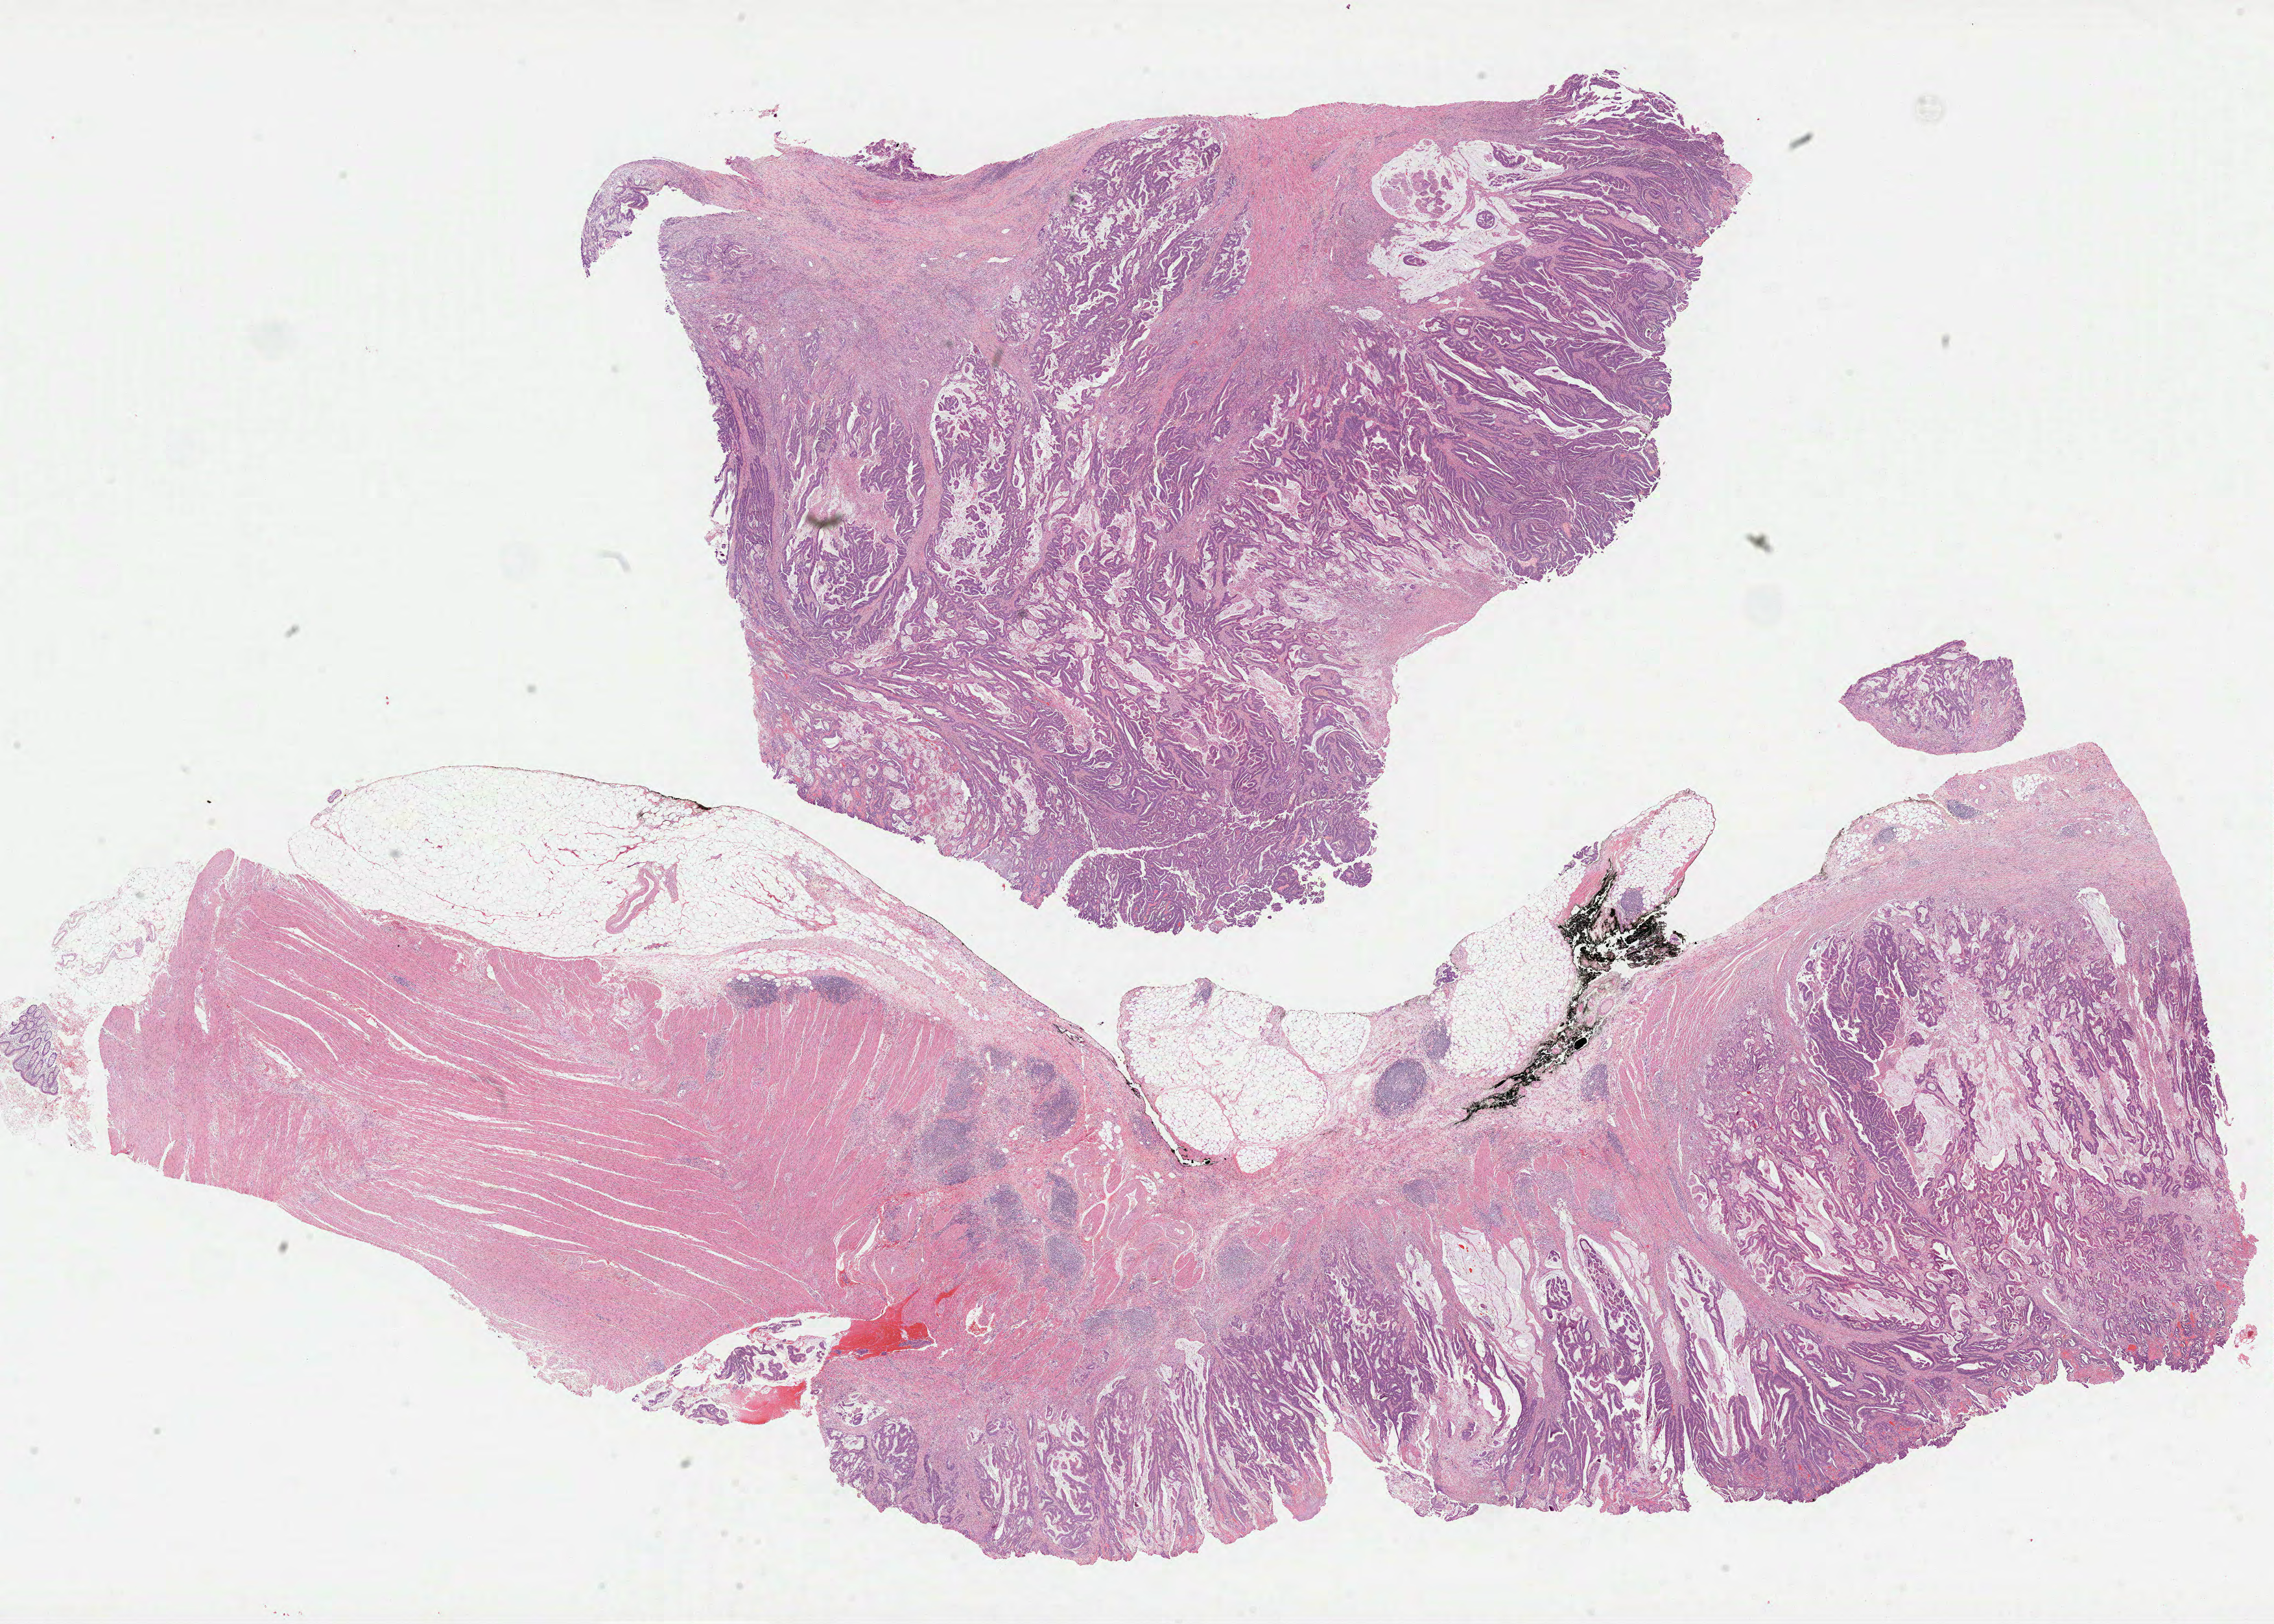
Hematoxylin and eosin (H&E) stained whole-slide image, whole scanned area (about 28.3 x 20.2 mm) shown as a low-resolution overview. FFPE section. Primary tumour sample from the colon. Female, age 58 years at initial diagnosis.
TNM: T3 N0 M0. AJCC pathologic stage: IIA (6th edition). Histologic diagnosis: Adenocarcinoma, NOS (cecum).